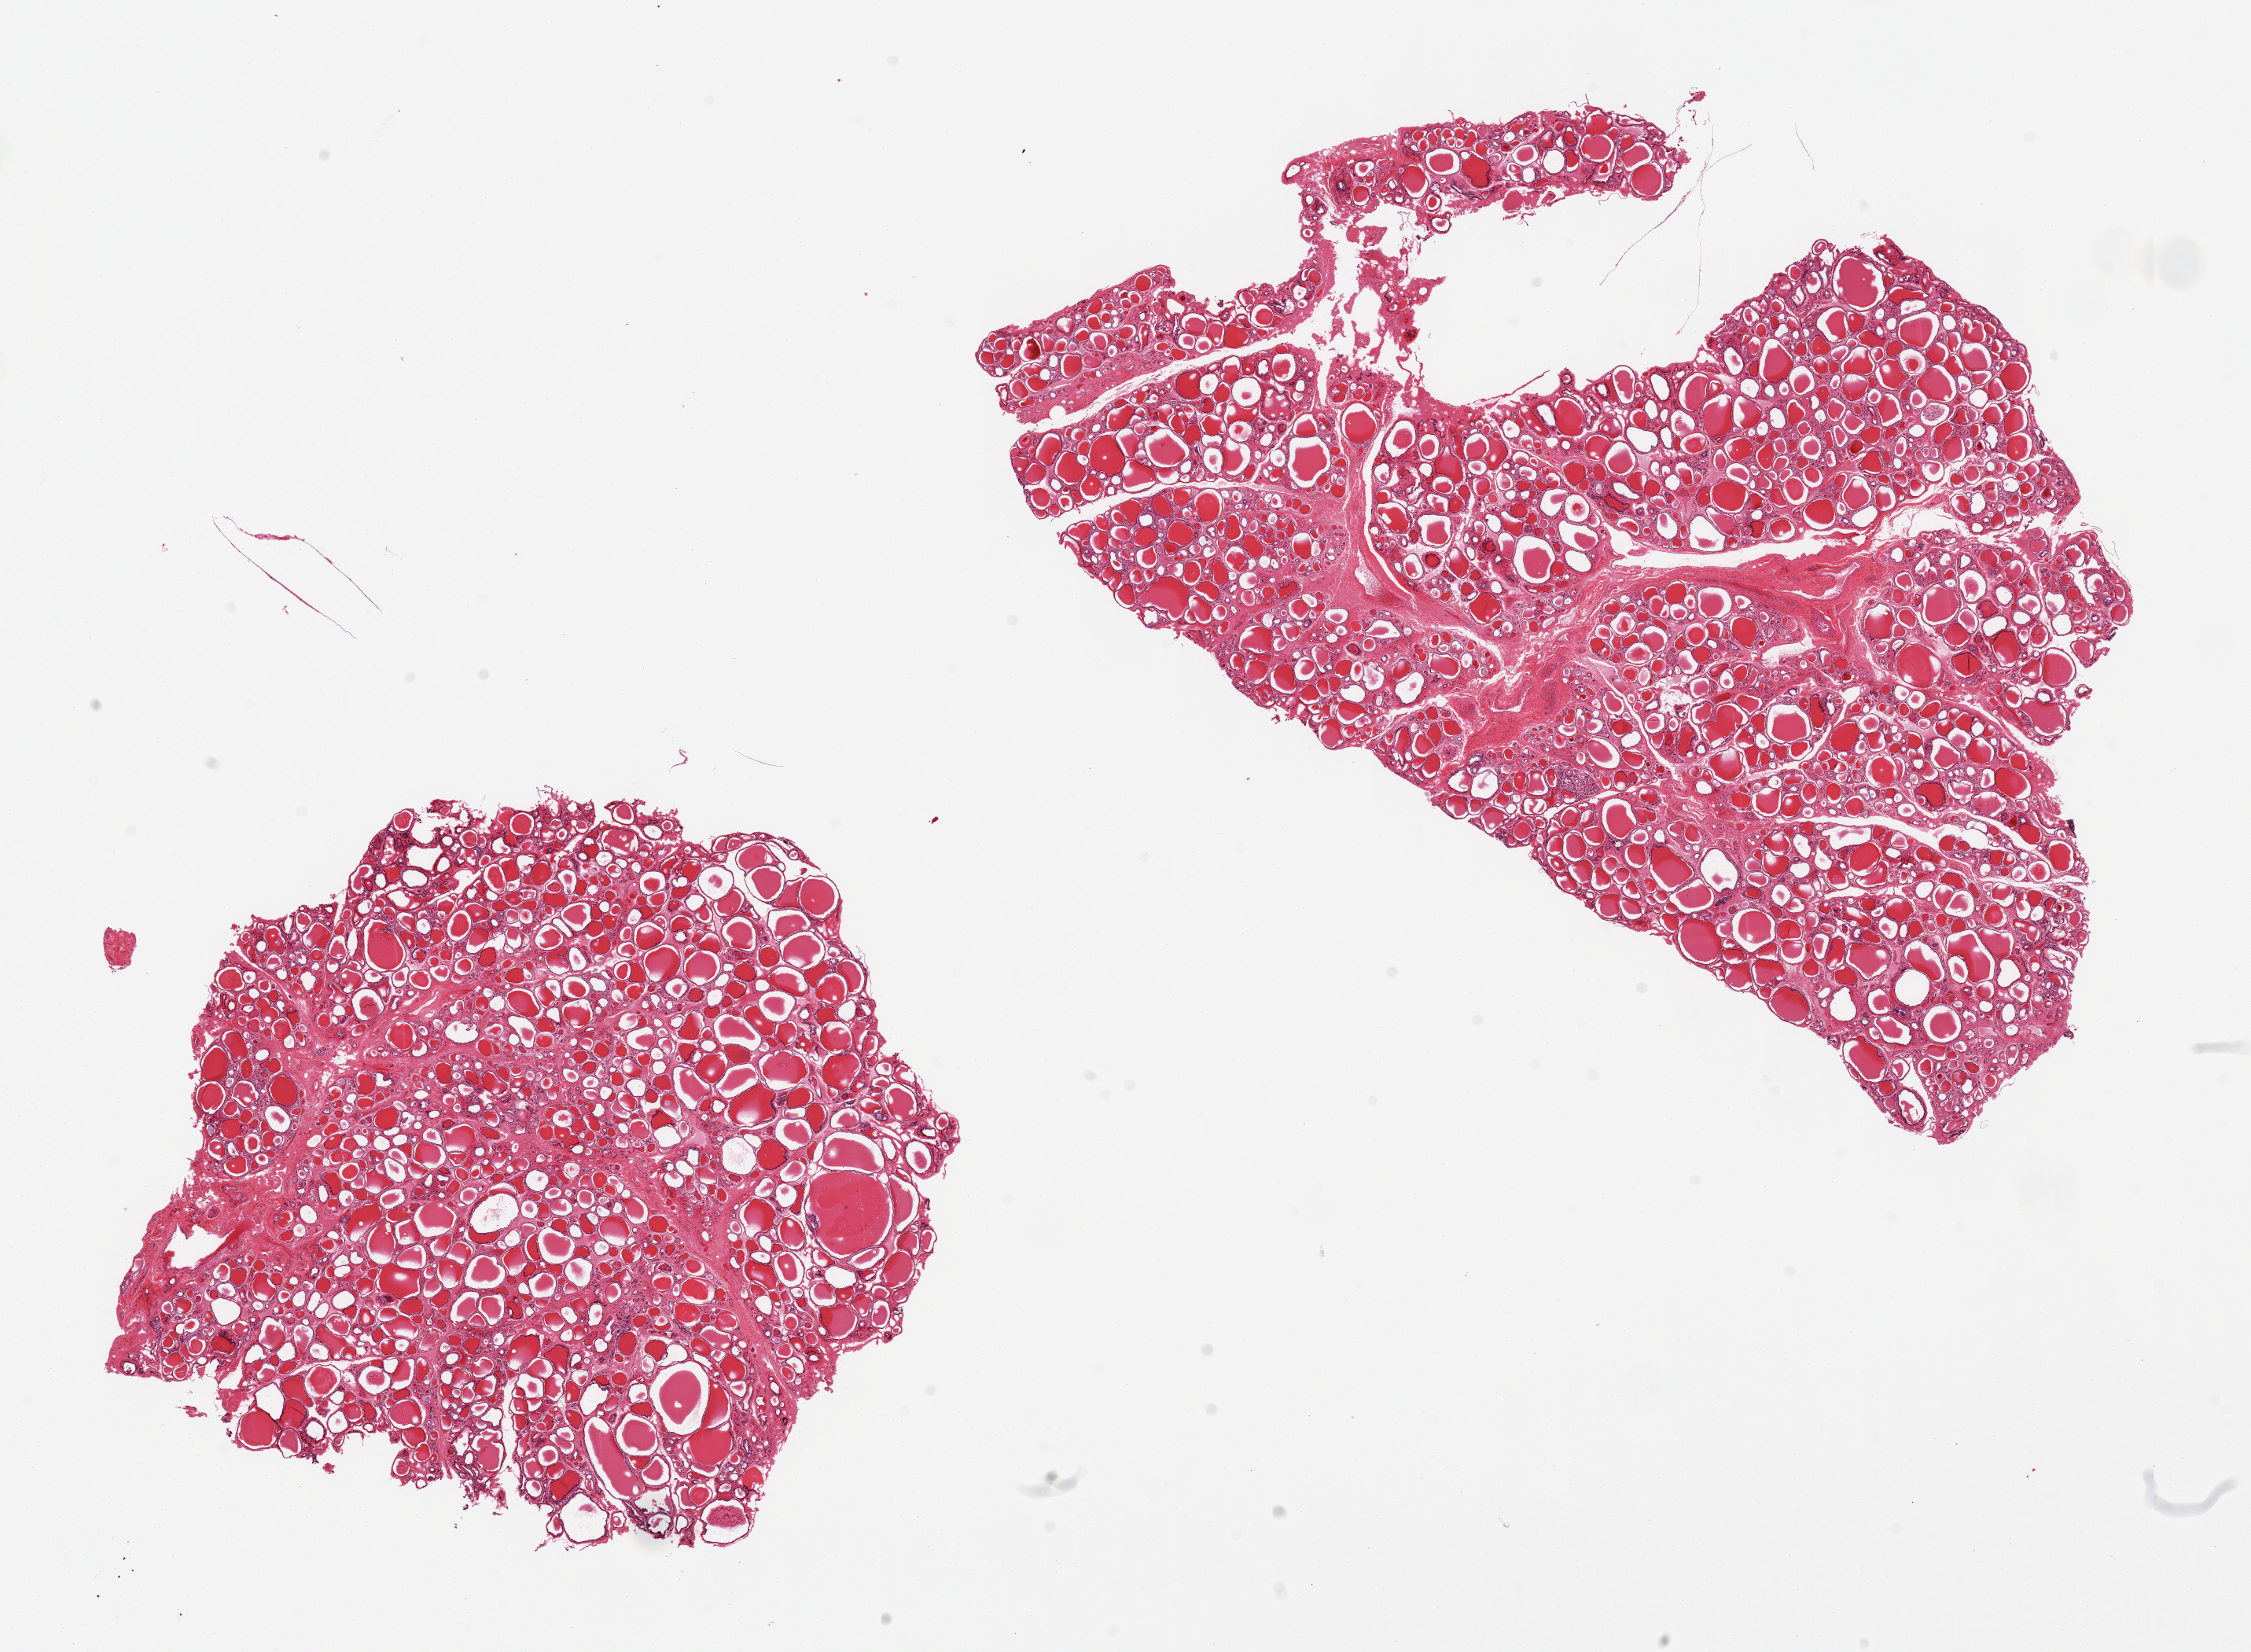
H&E whole-slide image, brightfield — a low-resolution overview of the entire scanned area, about 22.6 x 16.6 mm (acquisition: 20x scan); PAXgene-fixed, paraffin-embedded tissue; section of thyroid (target tissue); donor tissue sample.
- review note (as recorded): 2 pieces